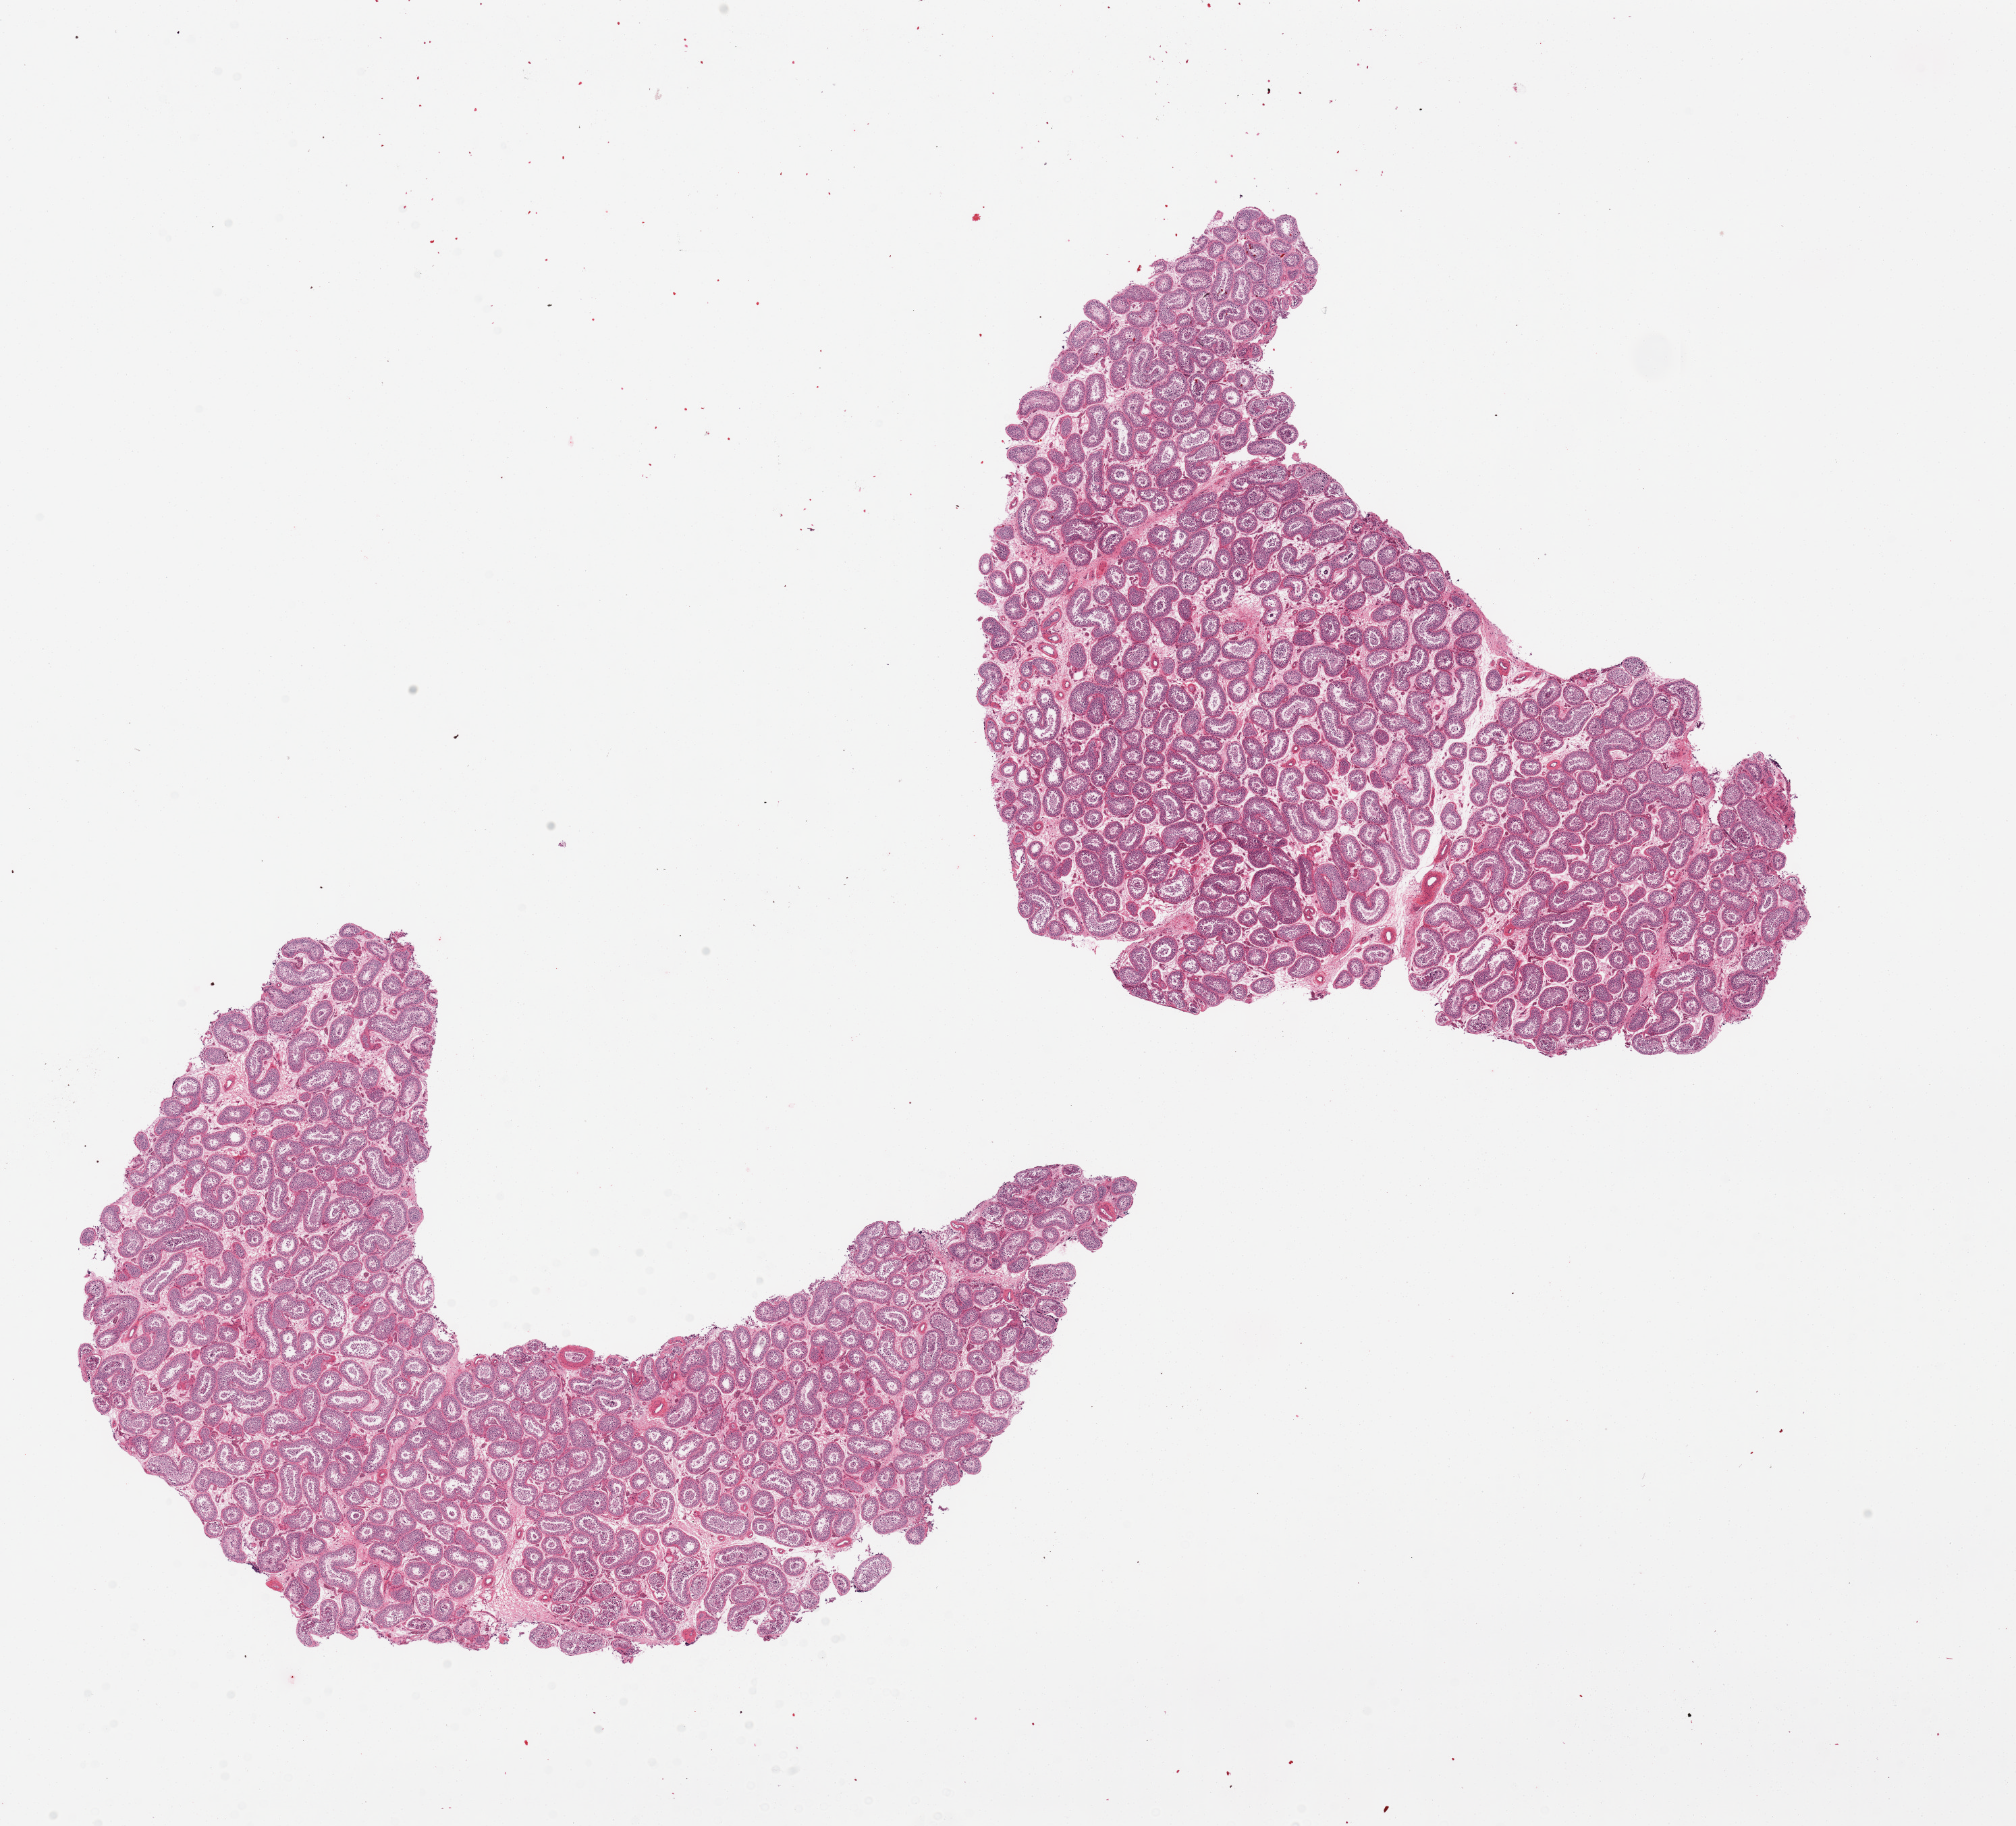
Digitized hematoxylin and eosin (H&E)-stained section, brightfield, low-resolution overview of the scanned area, about 23.6 x 21.4 mm, PAXgene-fixed paraffin-embedded (PFPE) section, sampled site (target tissue): testis, tissue donor sample. Donor: male.
• reviewer comment on this tissue sample: 2 pieces, sprematogenesis is present